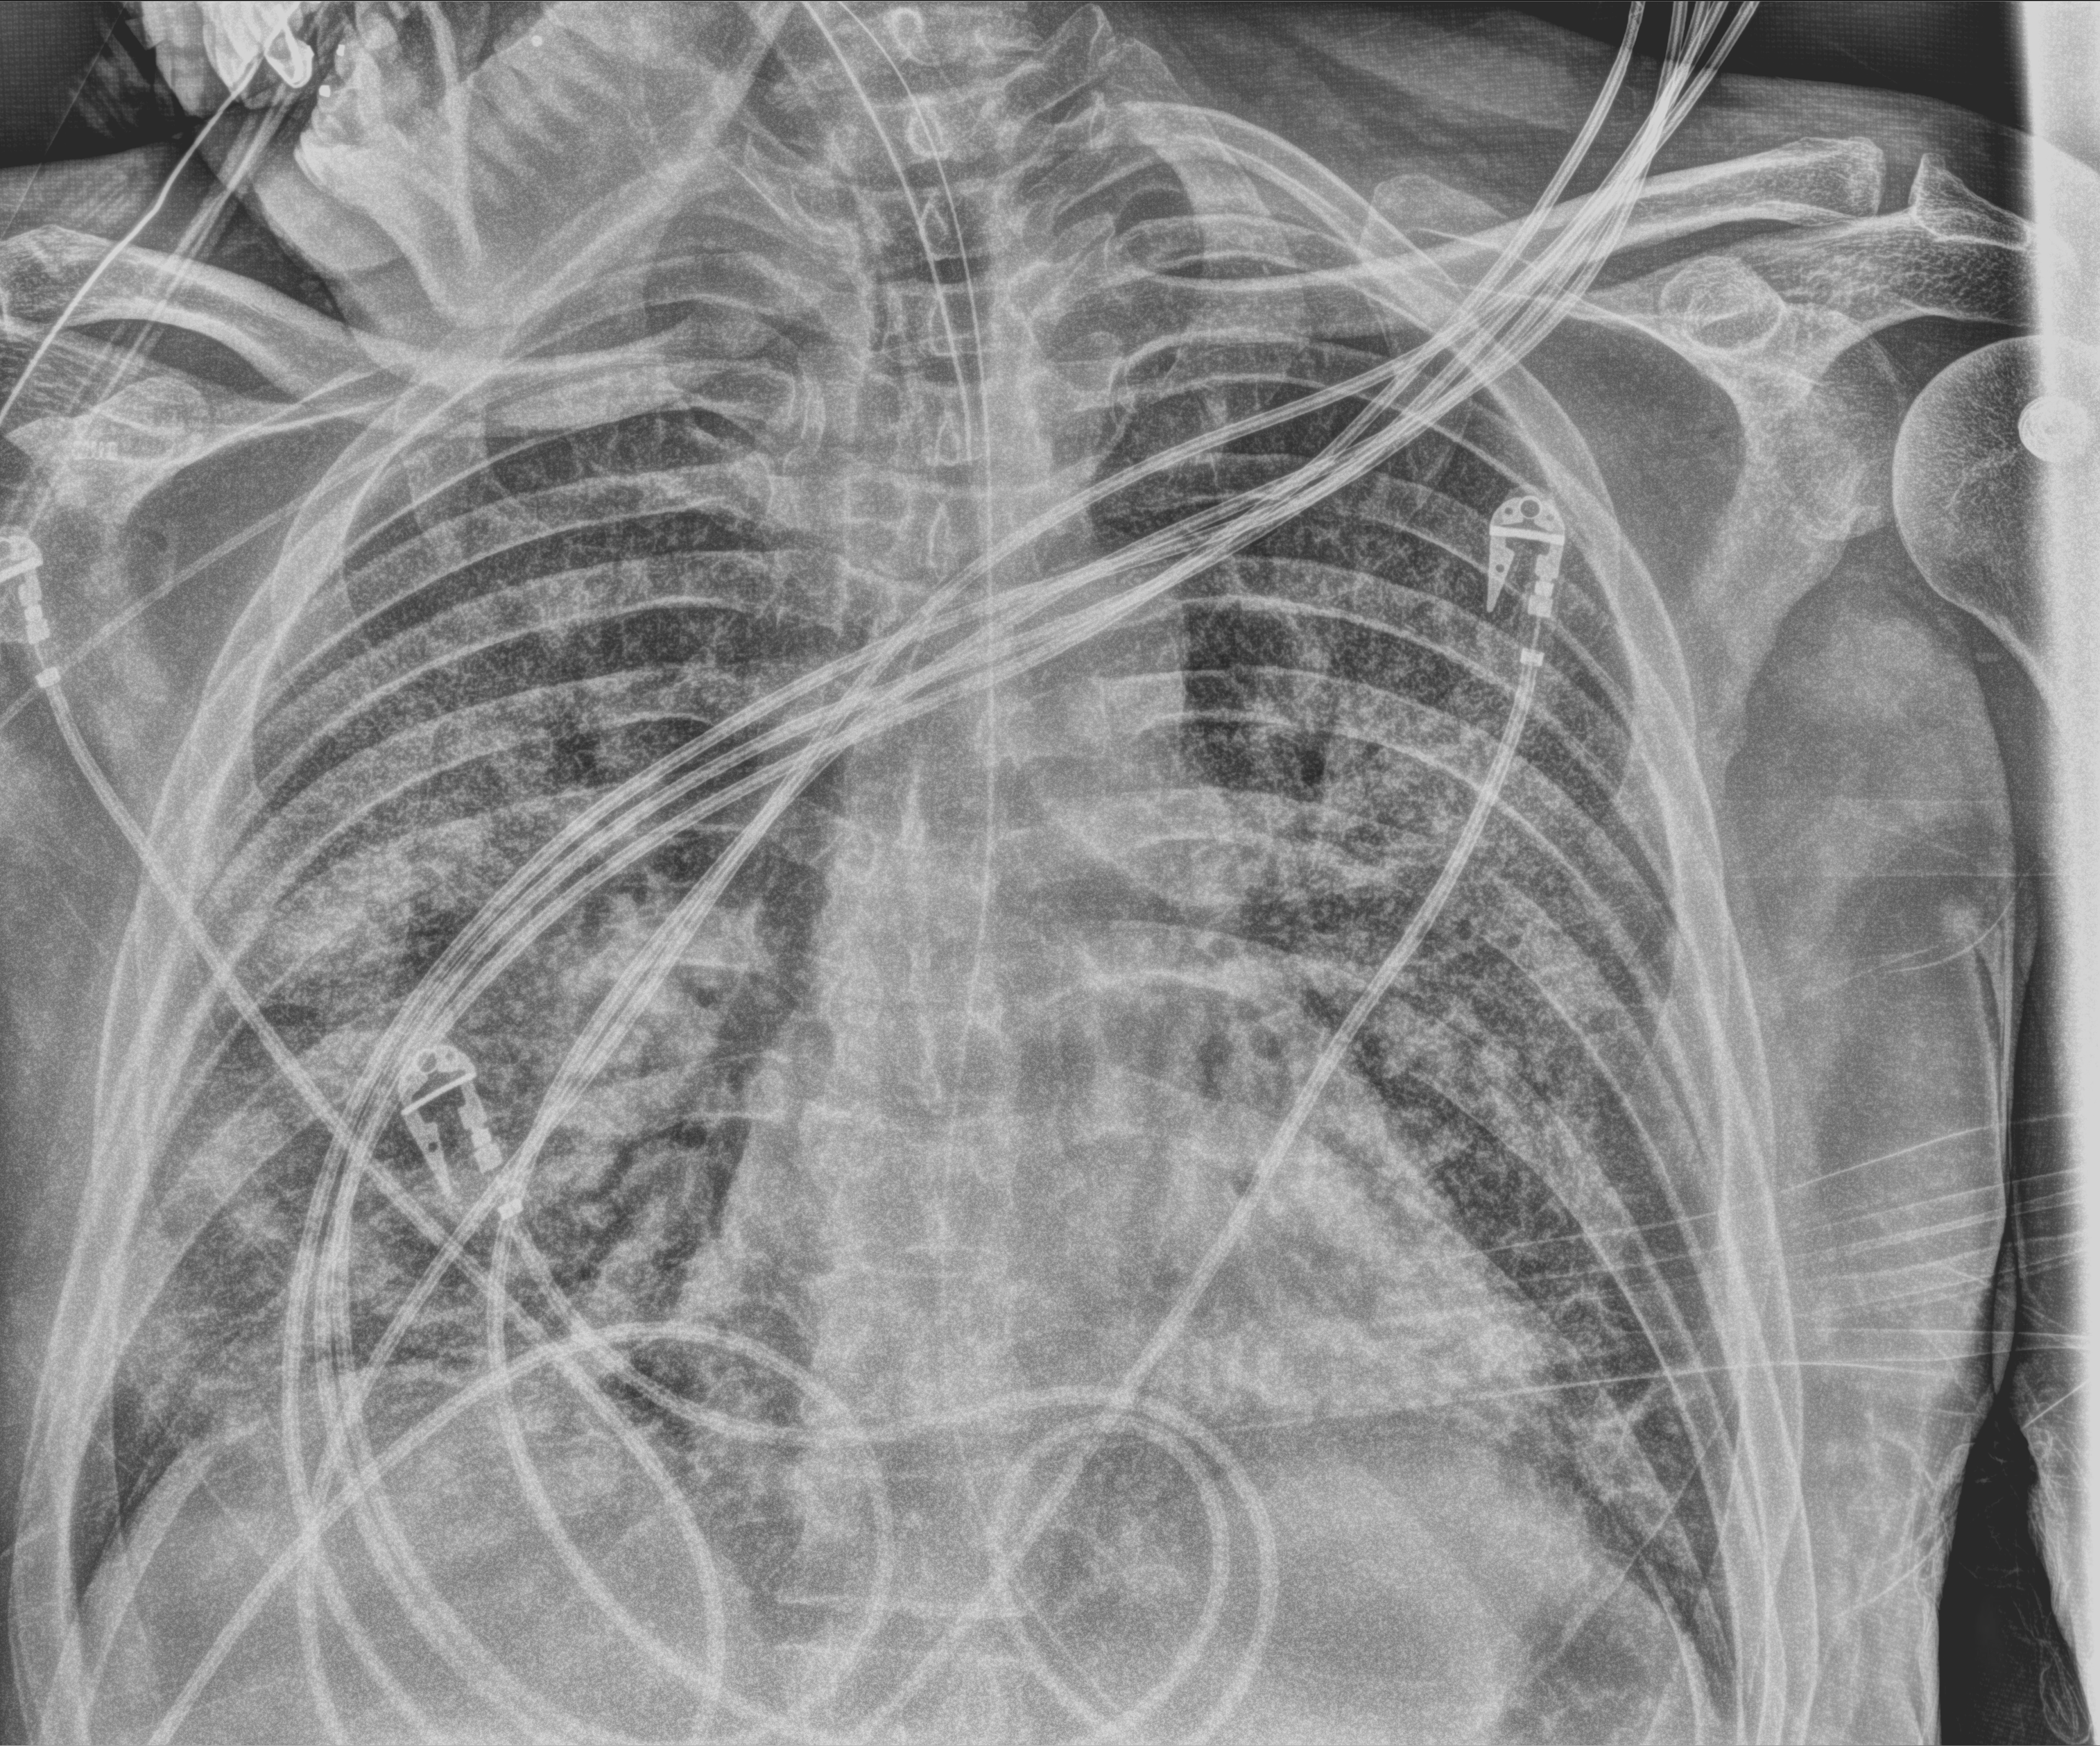
Portable chest radiograph; anteroposterior (AP) projection. Male patient hospitalised with COVID-19, age 18–59 years.
From the hospital-stay record, not from the radiograph (when in the stay this image was taken is not recorded):
- admitted to intensive care during this hospital stay: yes